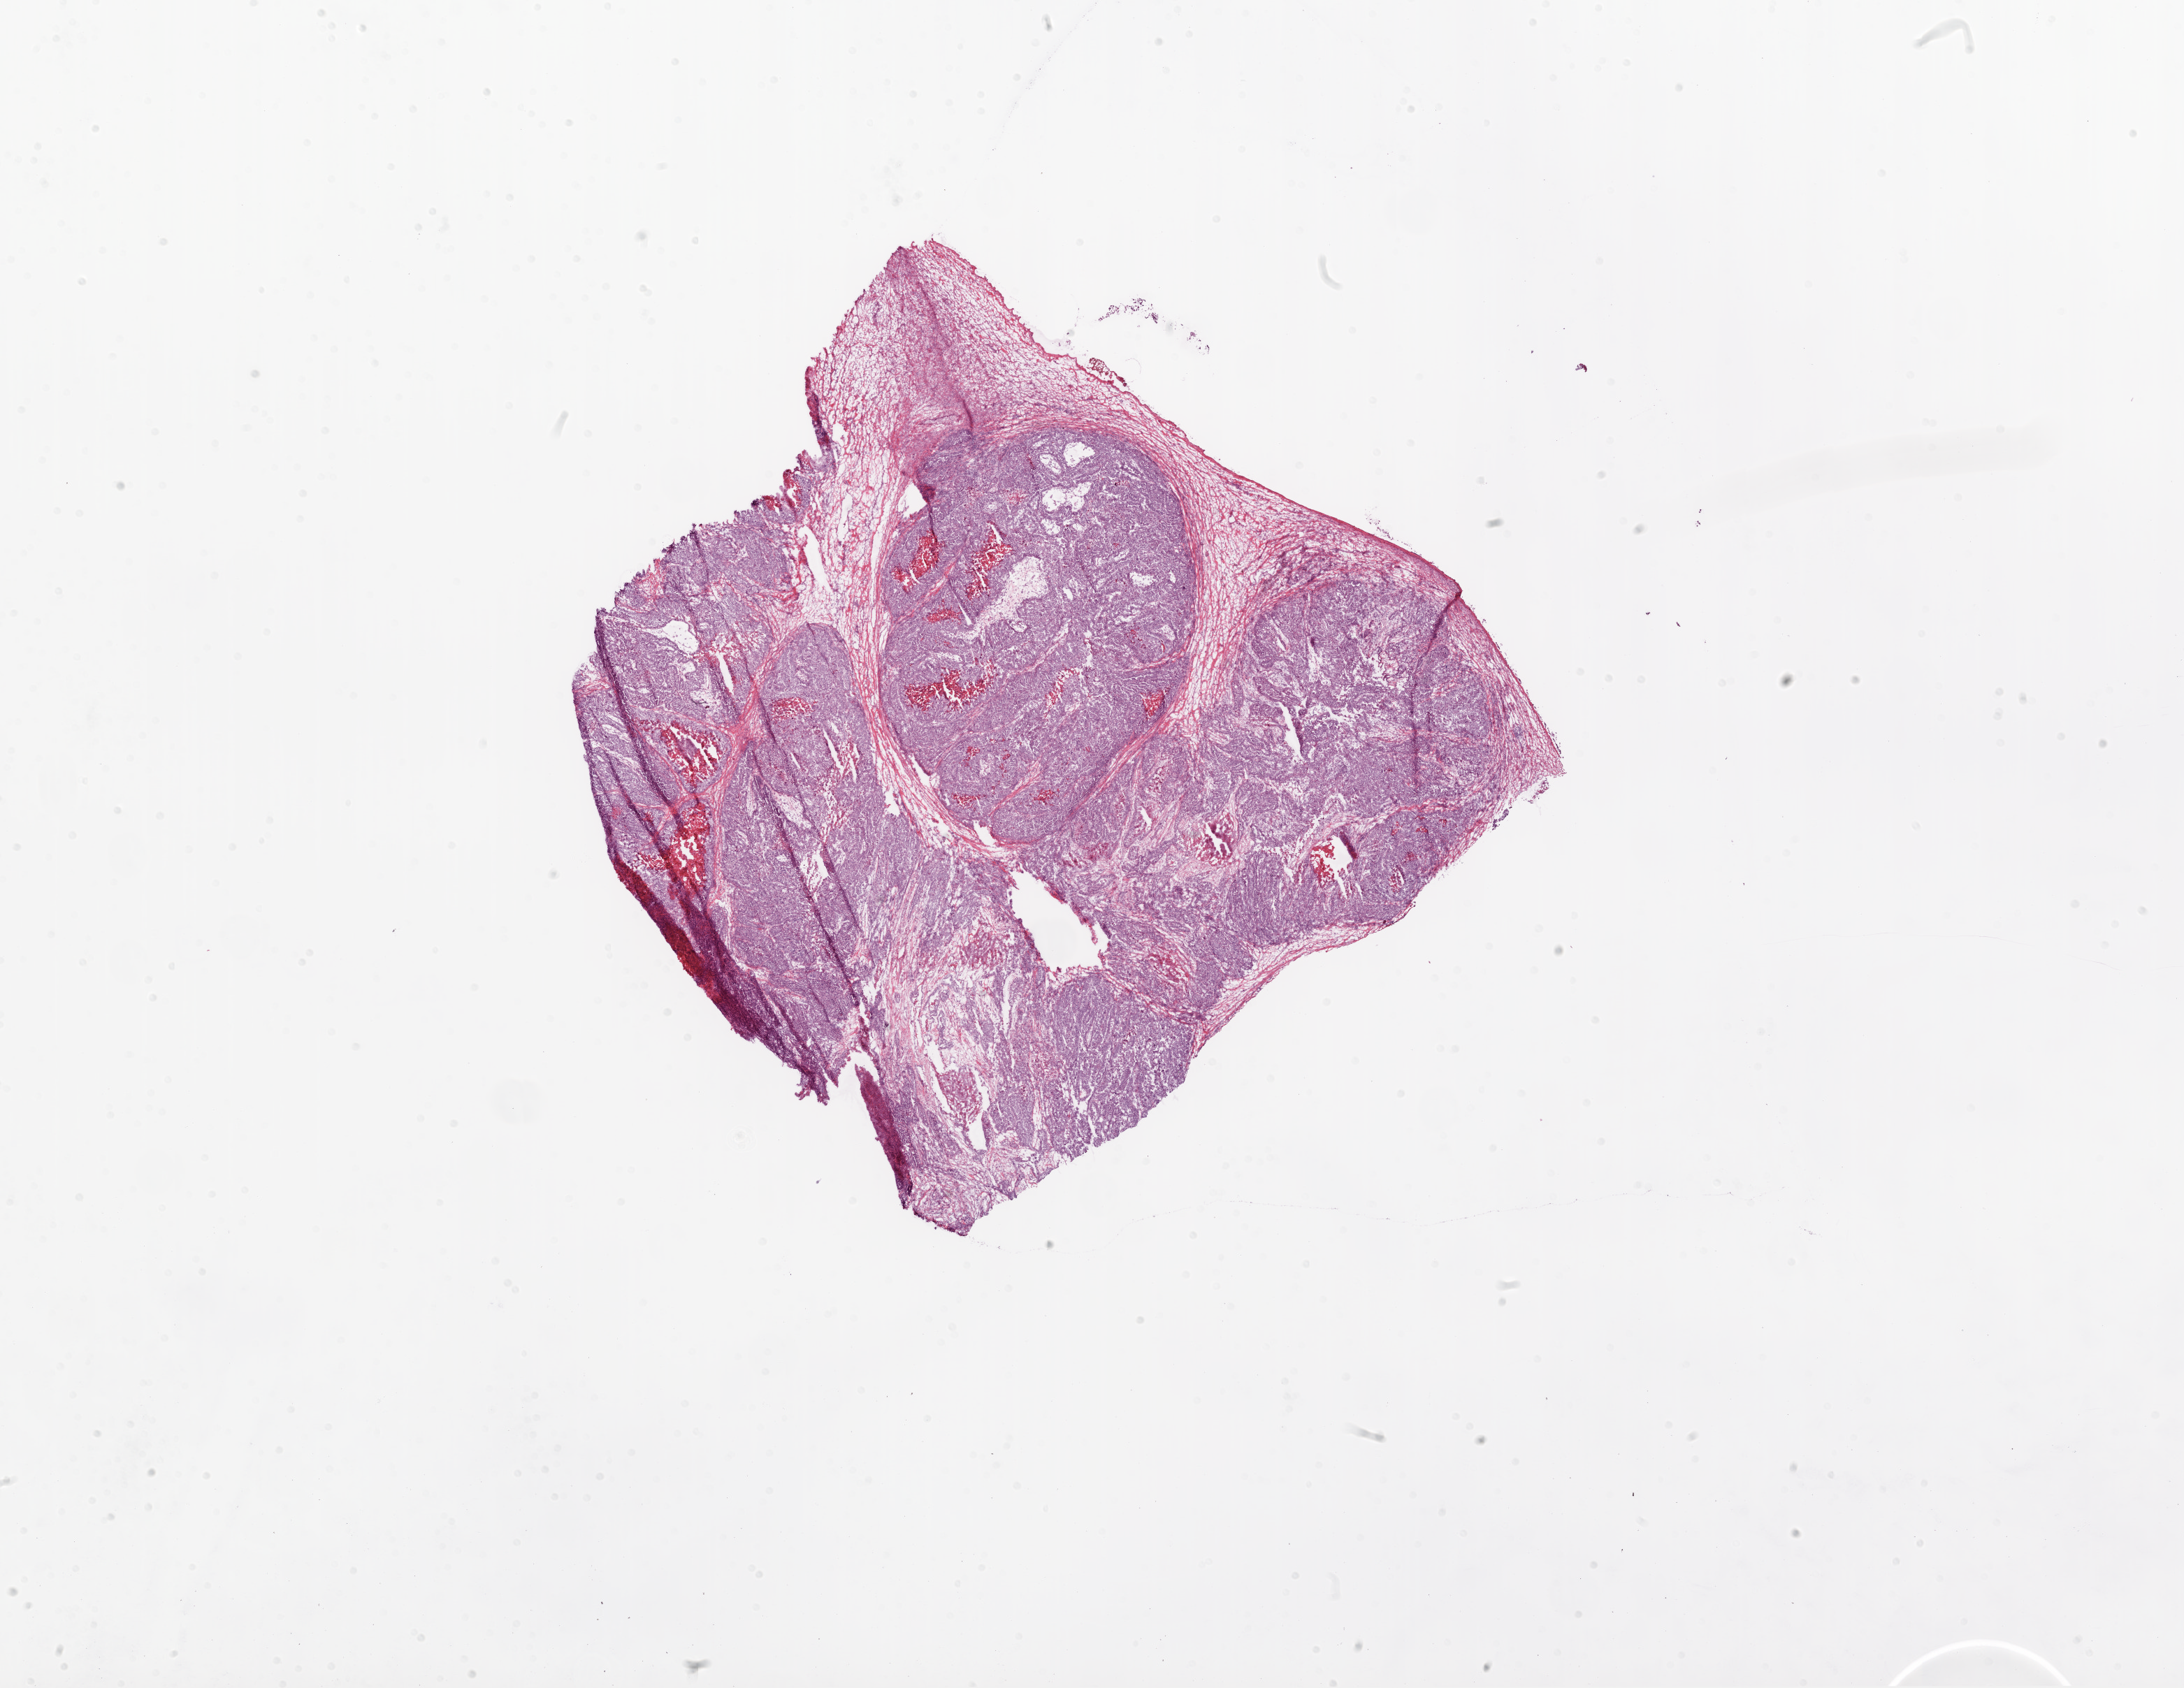
Whole-slide histology image, H&E-stained — whole scanned area (about 25.1 x 19.4 mm) shown as a low-resolution overview, frozen section from the bottom of the tissue portion, primary tumour sample from the ovary. Female, age 81 years at initial diagnosis. Histologic grade: G2 (moderately differentiated). Slide review estimates, as recorded: tumour cells 80%, tumour nuclei 90%, normal cells 0%, stromal cells 10%, necrosis 10%.
FIGO stage: IIC. Diagnosis: Serous cystadenocarcinoma, NOS.